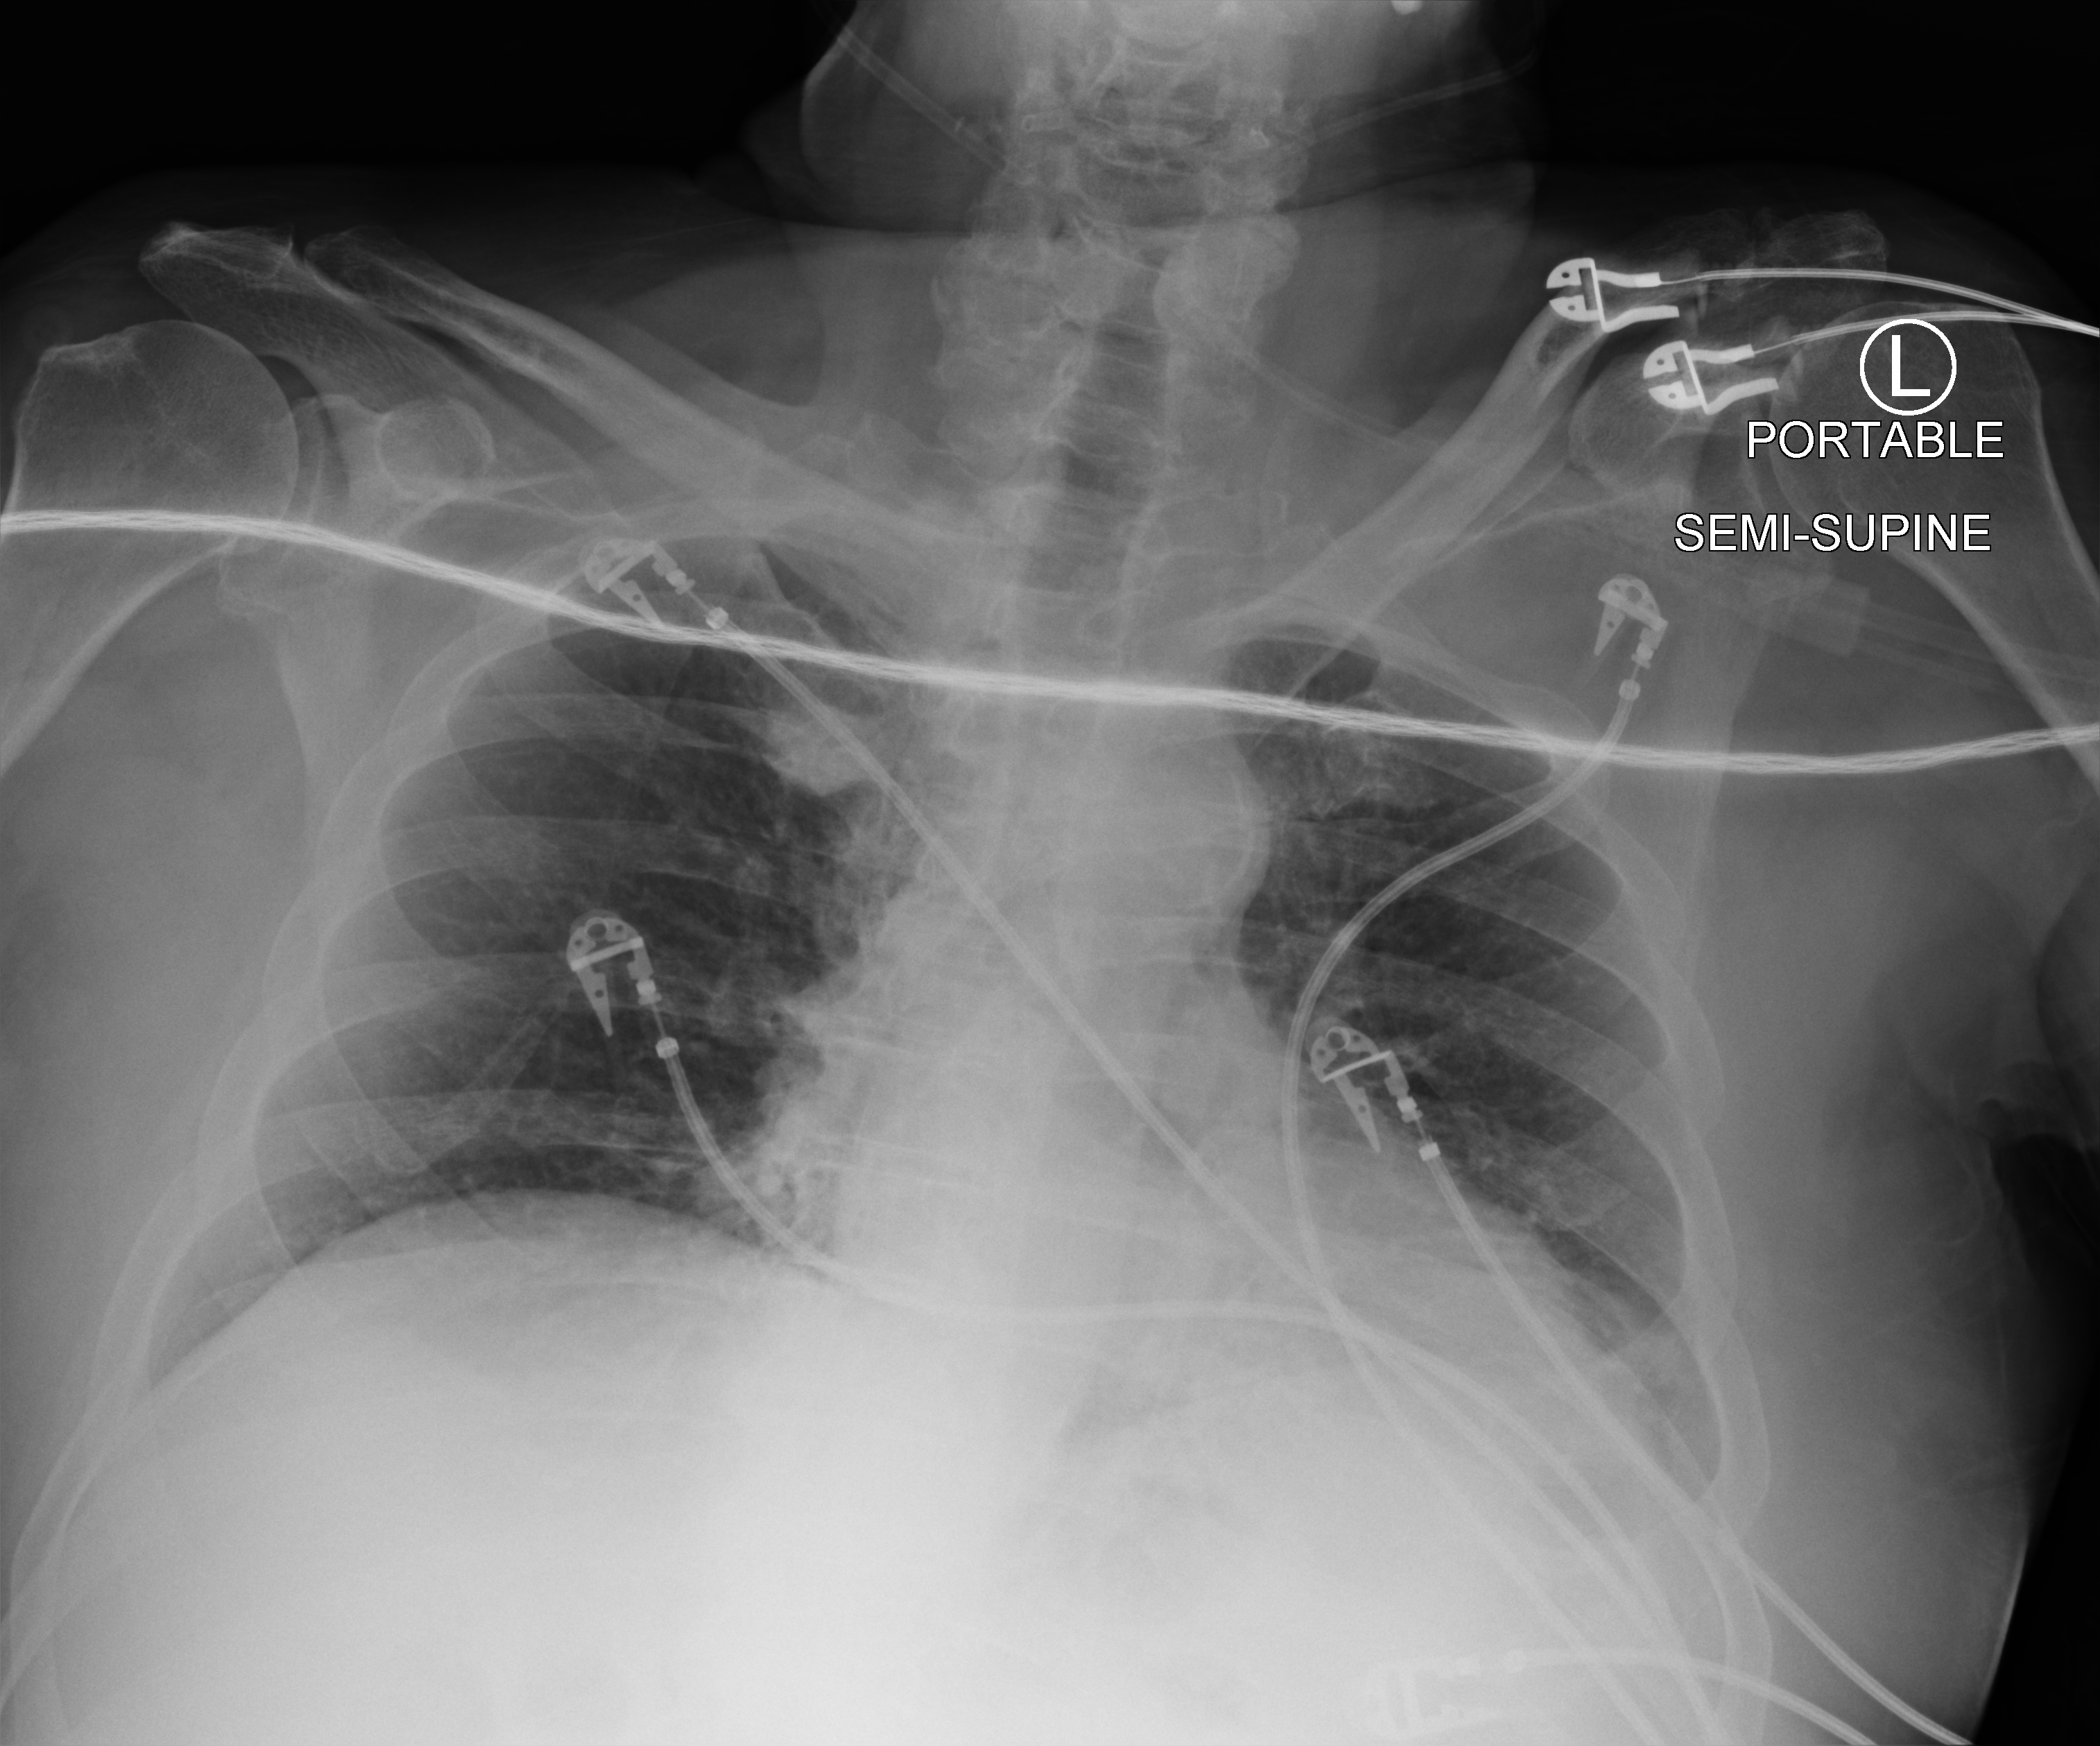
Chest X-ray (portable), anteroposterior (AP) projection. Male patient hospitalised with COVID-19, age 75–90 years.
From the hospital-stay record, not from the radiograph (when in the stay this image was taken is not recorded):
- admitted to intensive care during this hospital stay: no